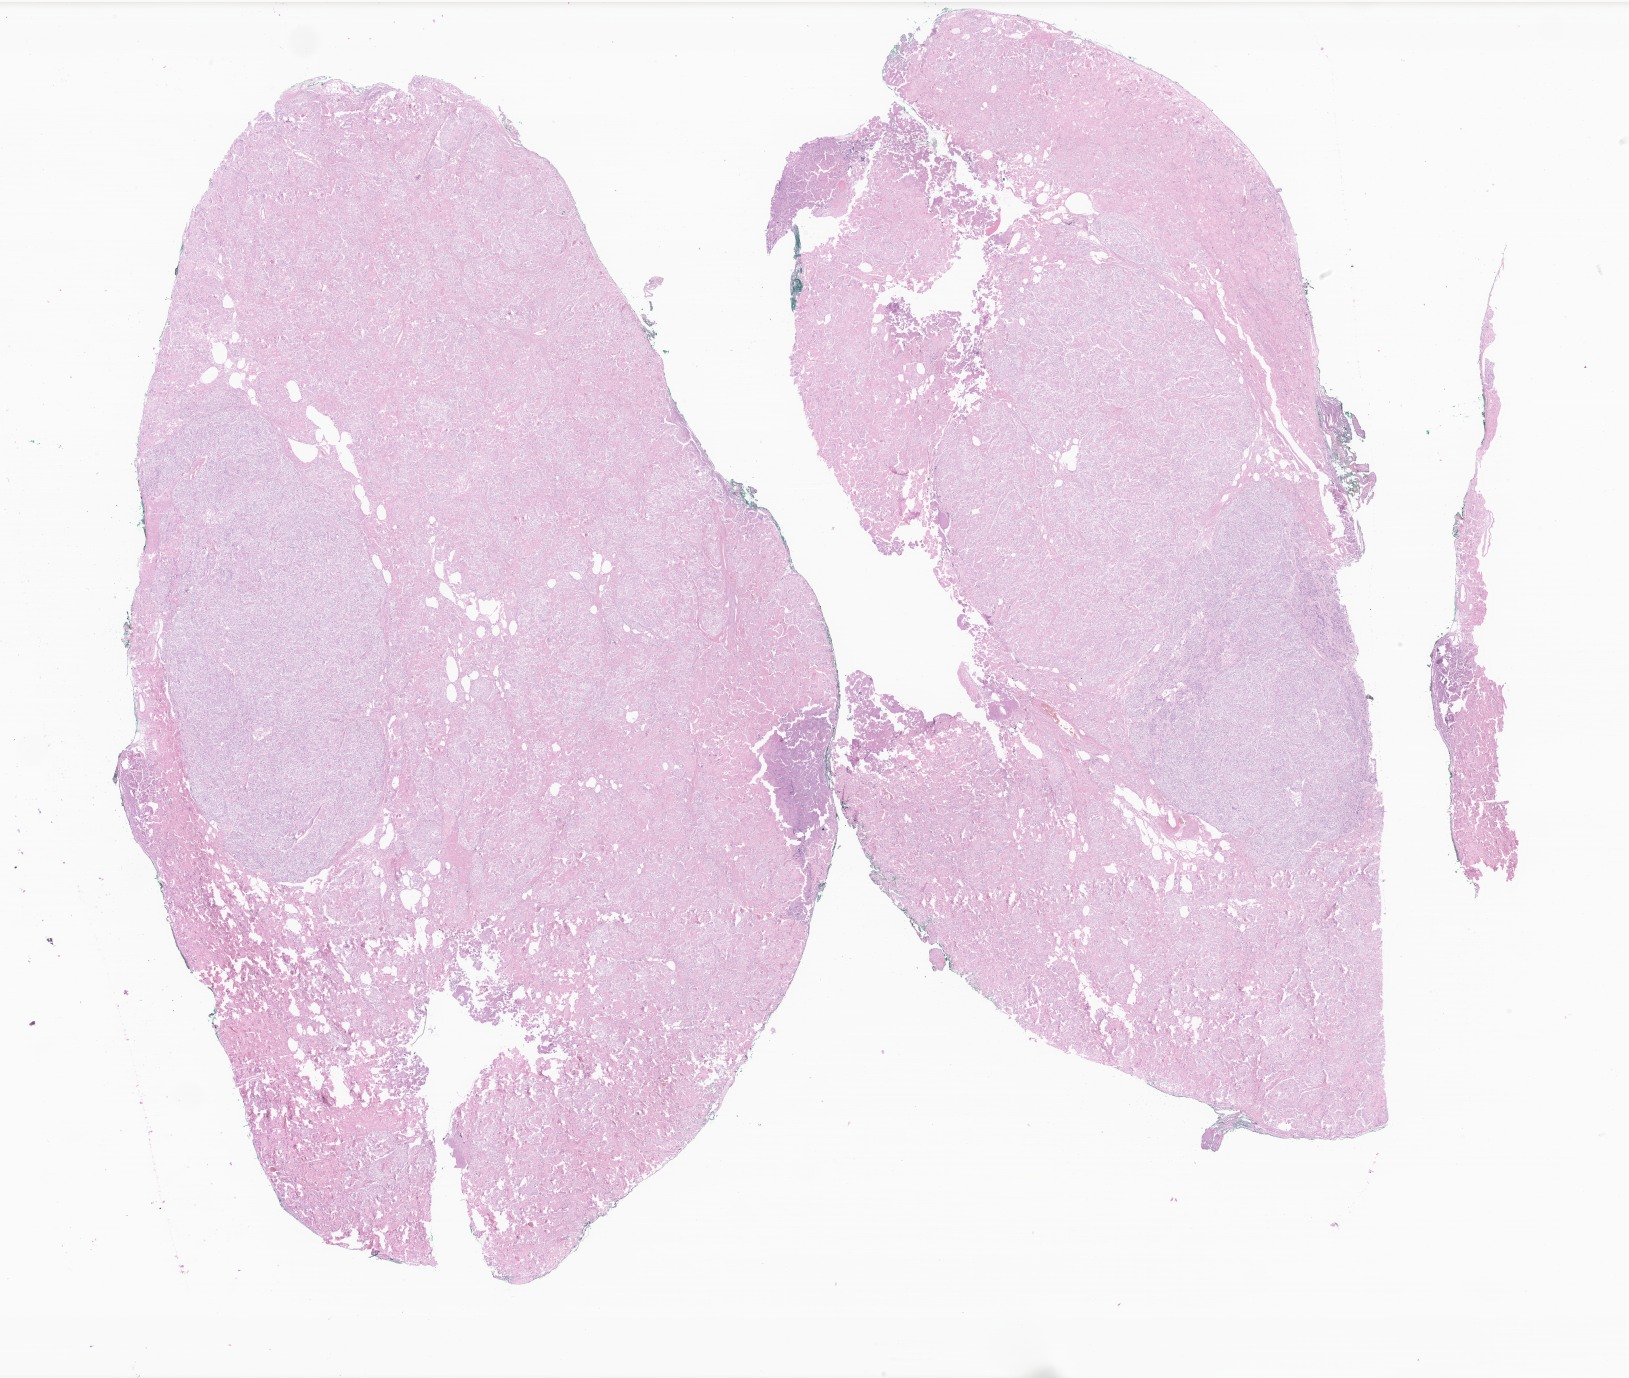
Whole-slide image, hematoxylin and eosin (H&E) stain of tumor tissue from the spinal cord, low-resolution overview of the scanned area, about 27.5 x 23.2 mm; formalin-fixed, paraffin-embedded (FFPE) tissue. Patient: male, age 222 months (18 years 6 months).
Diagnosis (ICD-O-3 morphology term): Meningioma, NOS.